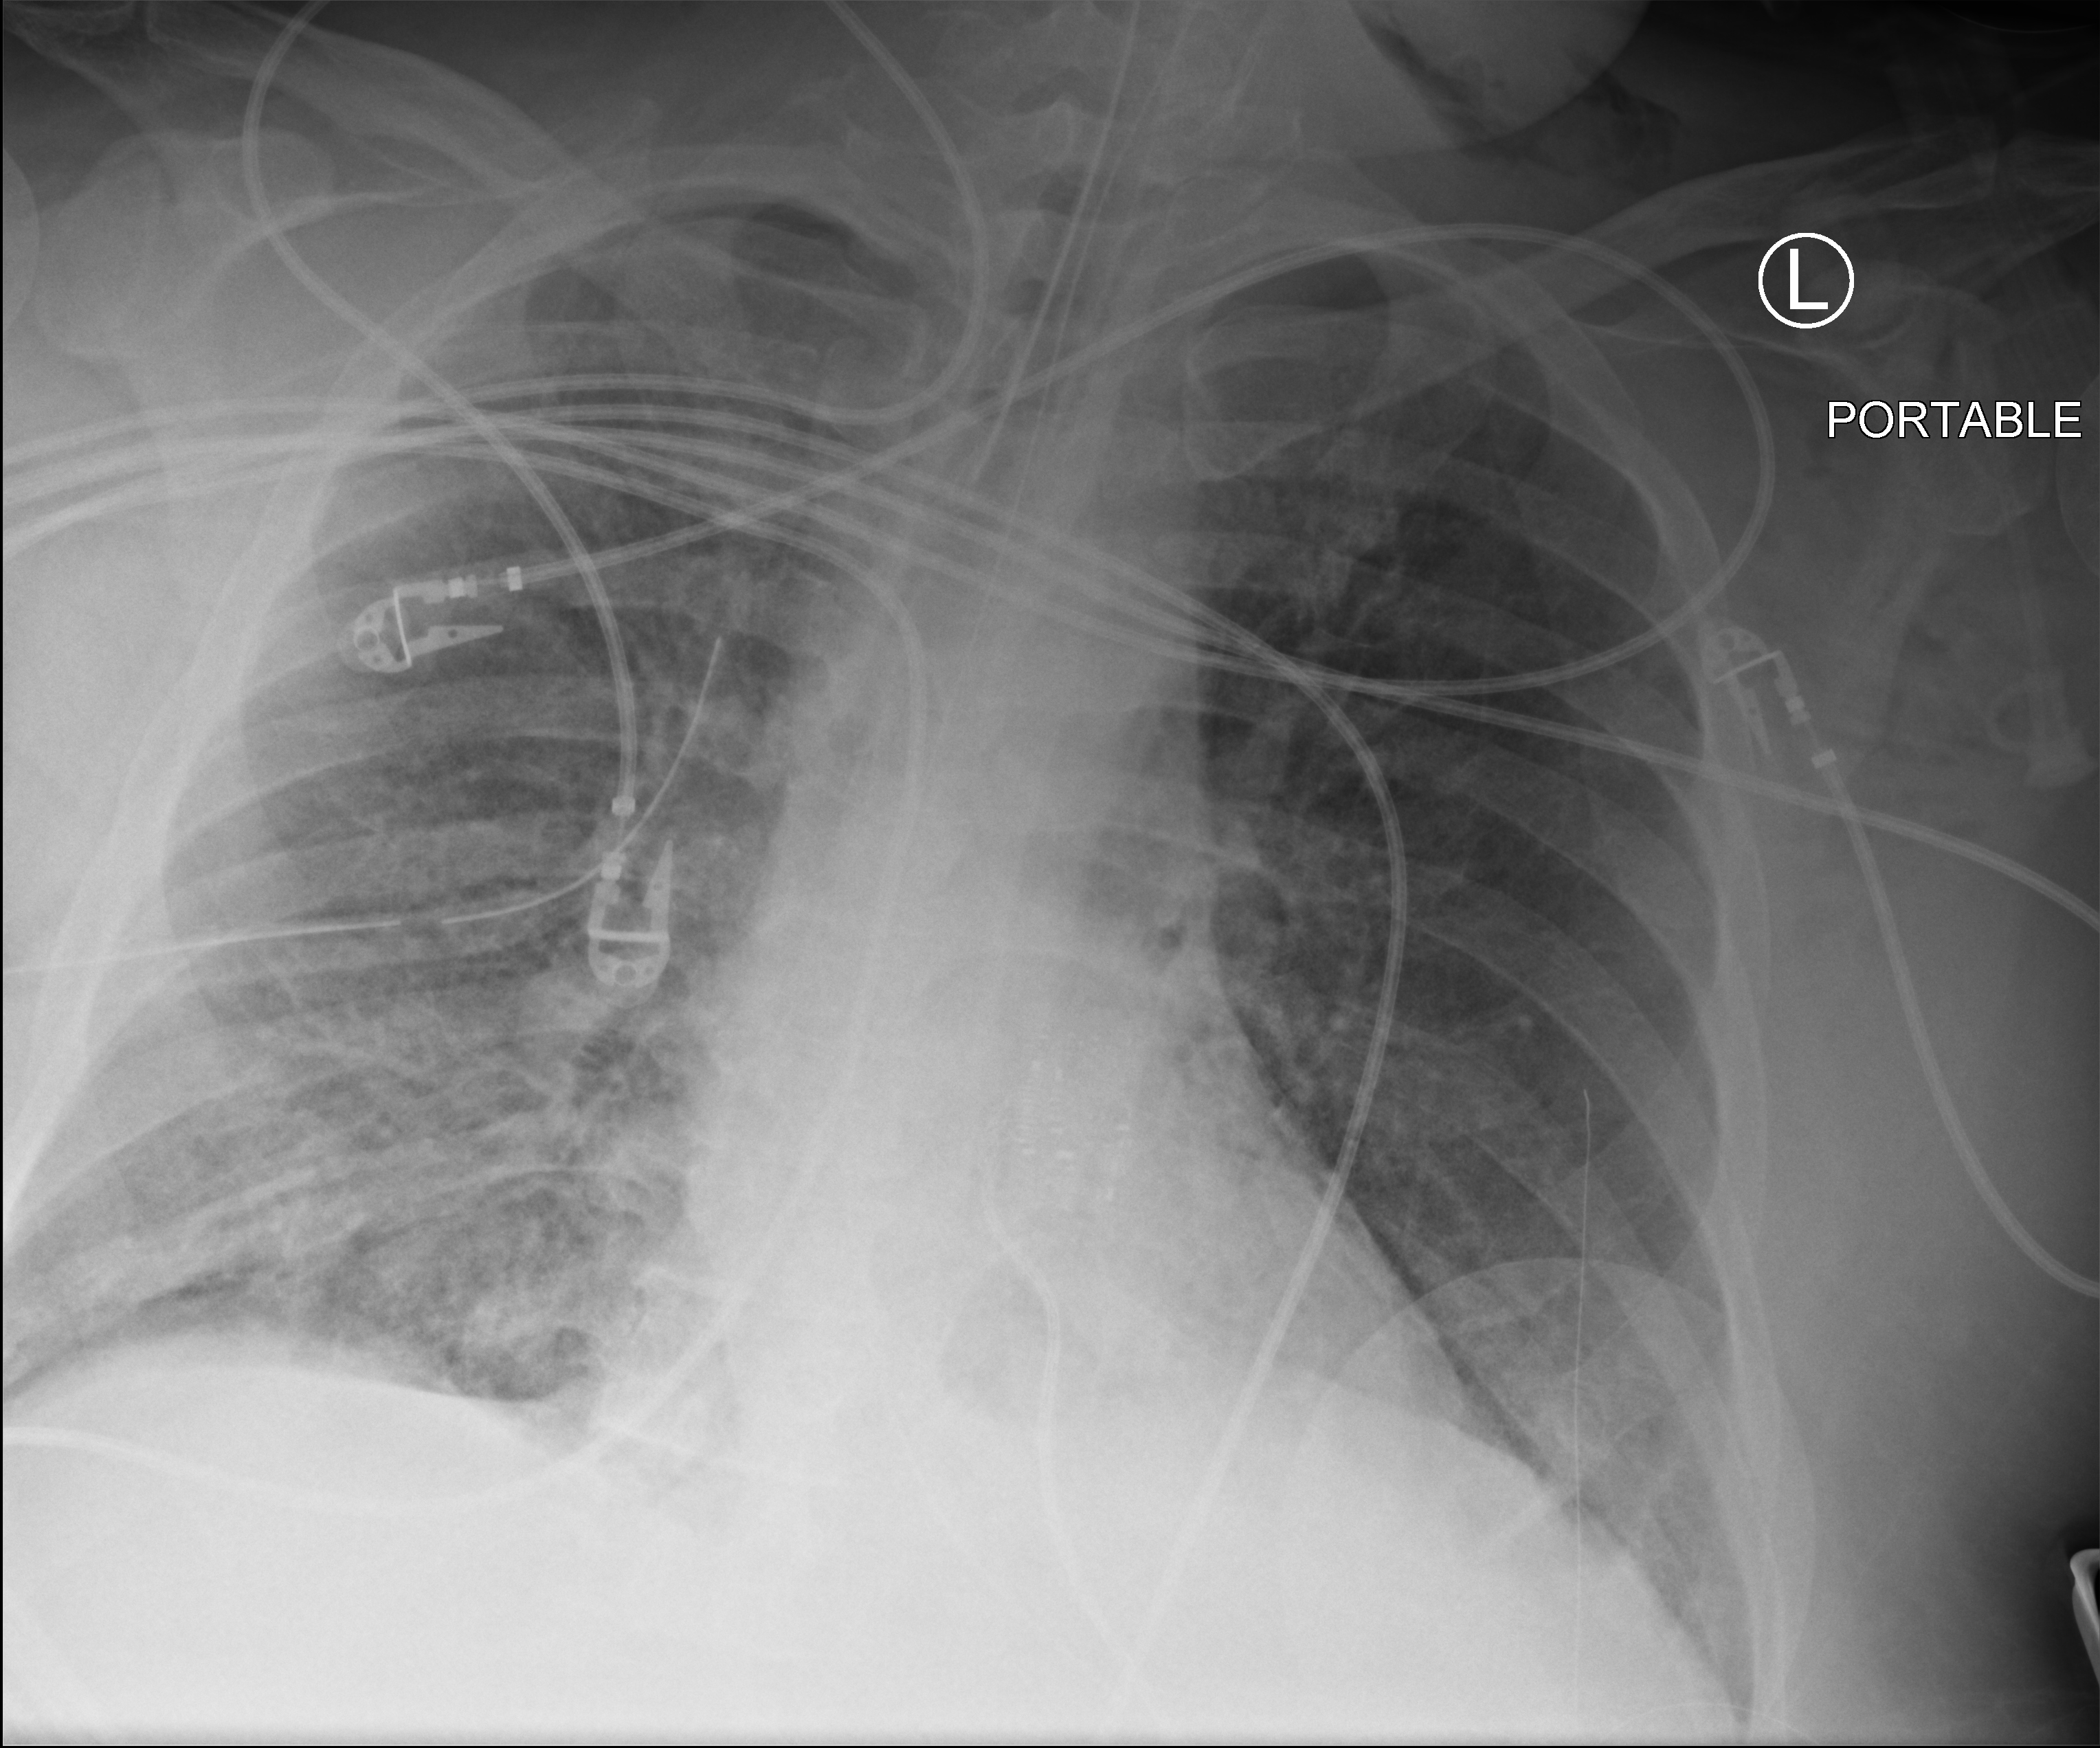
Bedside chest radiograph (computed radiography); anteroposterior (AP) projection. Adult patient hospitalised with COVID-19, age 18–59 years.
Admission-level facts for this patient (not findings on this image; timing relative to this image not recorded): admitted to intensive care during this hospital stay: yes; mechanically ventilated during this hospital stay: yes.